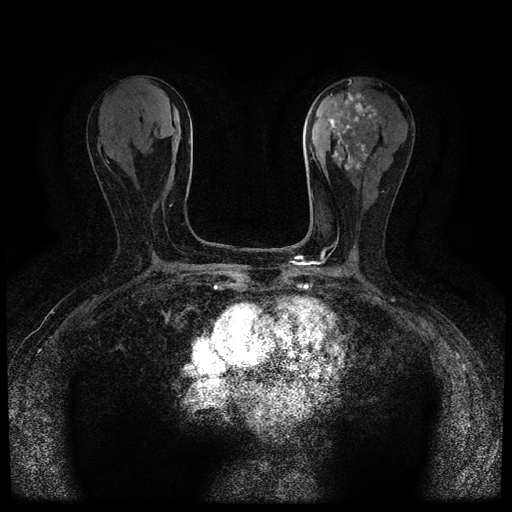
Breast MRI (dynamic contrast-enhanced, multi-phase), one axial slice. Position 38 of 116 along the scan axis. Dynamic contrast-enhanced series, time point 2 of 5 at this slice position (early post-contrast). 1.5 T. TE 2.7 ms, TR 5.4 ms. 512 × 512 image matrix, field of view 320 × 320 mm. Patient: female, 80 years.
Annotated regions visible in this slice (semi-automatic segmentation, software-assisted and operator-edited):
- breast lesion (labelled 'tumour' in the annotation; benign lesions carry a separate 'benign' label): box from (x=329, y=92) to (x=377, y=171) px